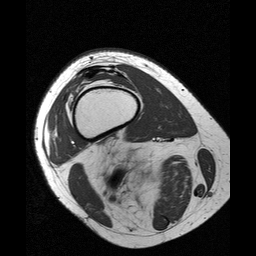
MRI of an extremity soft-tissue mass, one axial slice. Slice 24 of 25 in the series (ordered by position). 256 × 256 image matrix, field of view 160 × 160 mm. Female patient. Case-level facts recorded for this patient, not image findings: histological type: liposarcoma; site of the primary tumour: right thigh.
Annotated regions visible in this slice (manually delineated by an expert):
- gross tumour volume (mass): bounding box (x1, y1, x2, y2) in pixels: (124, 167, 163, 187)